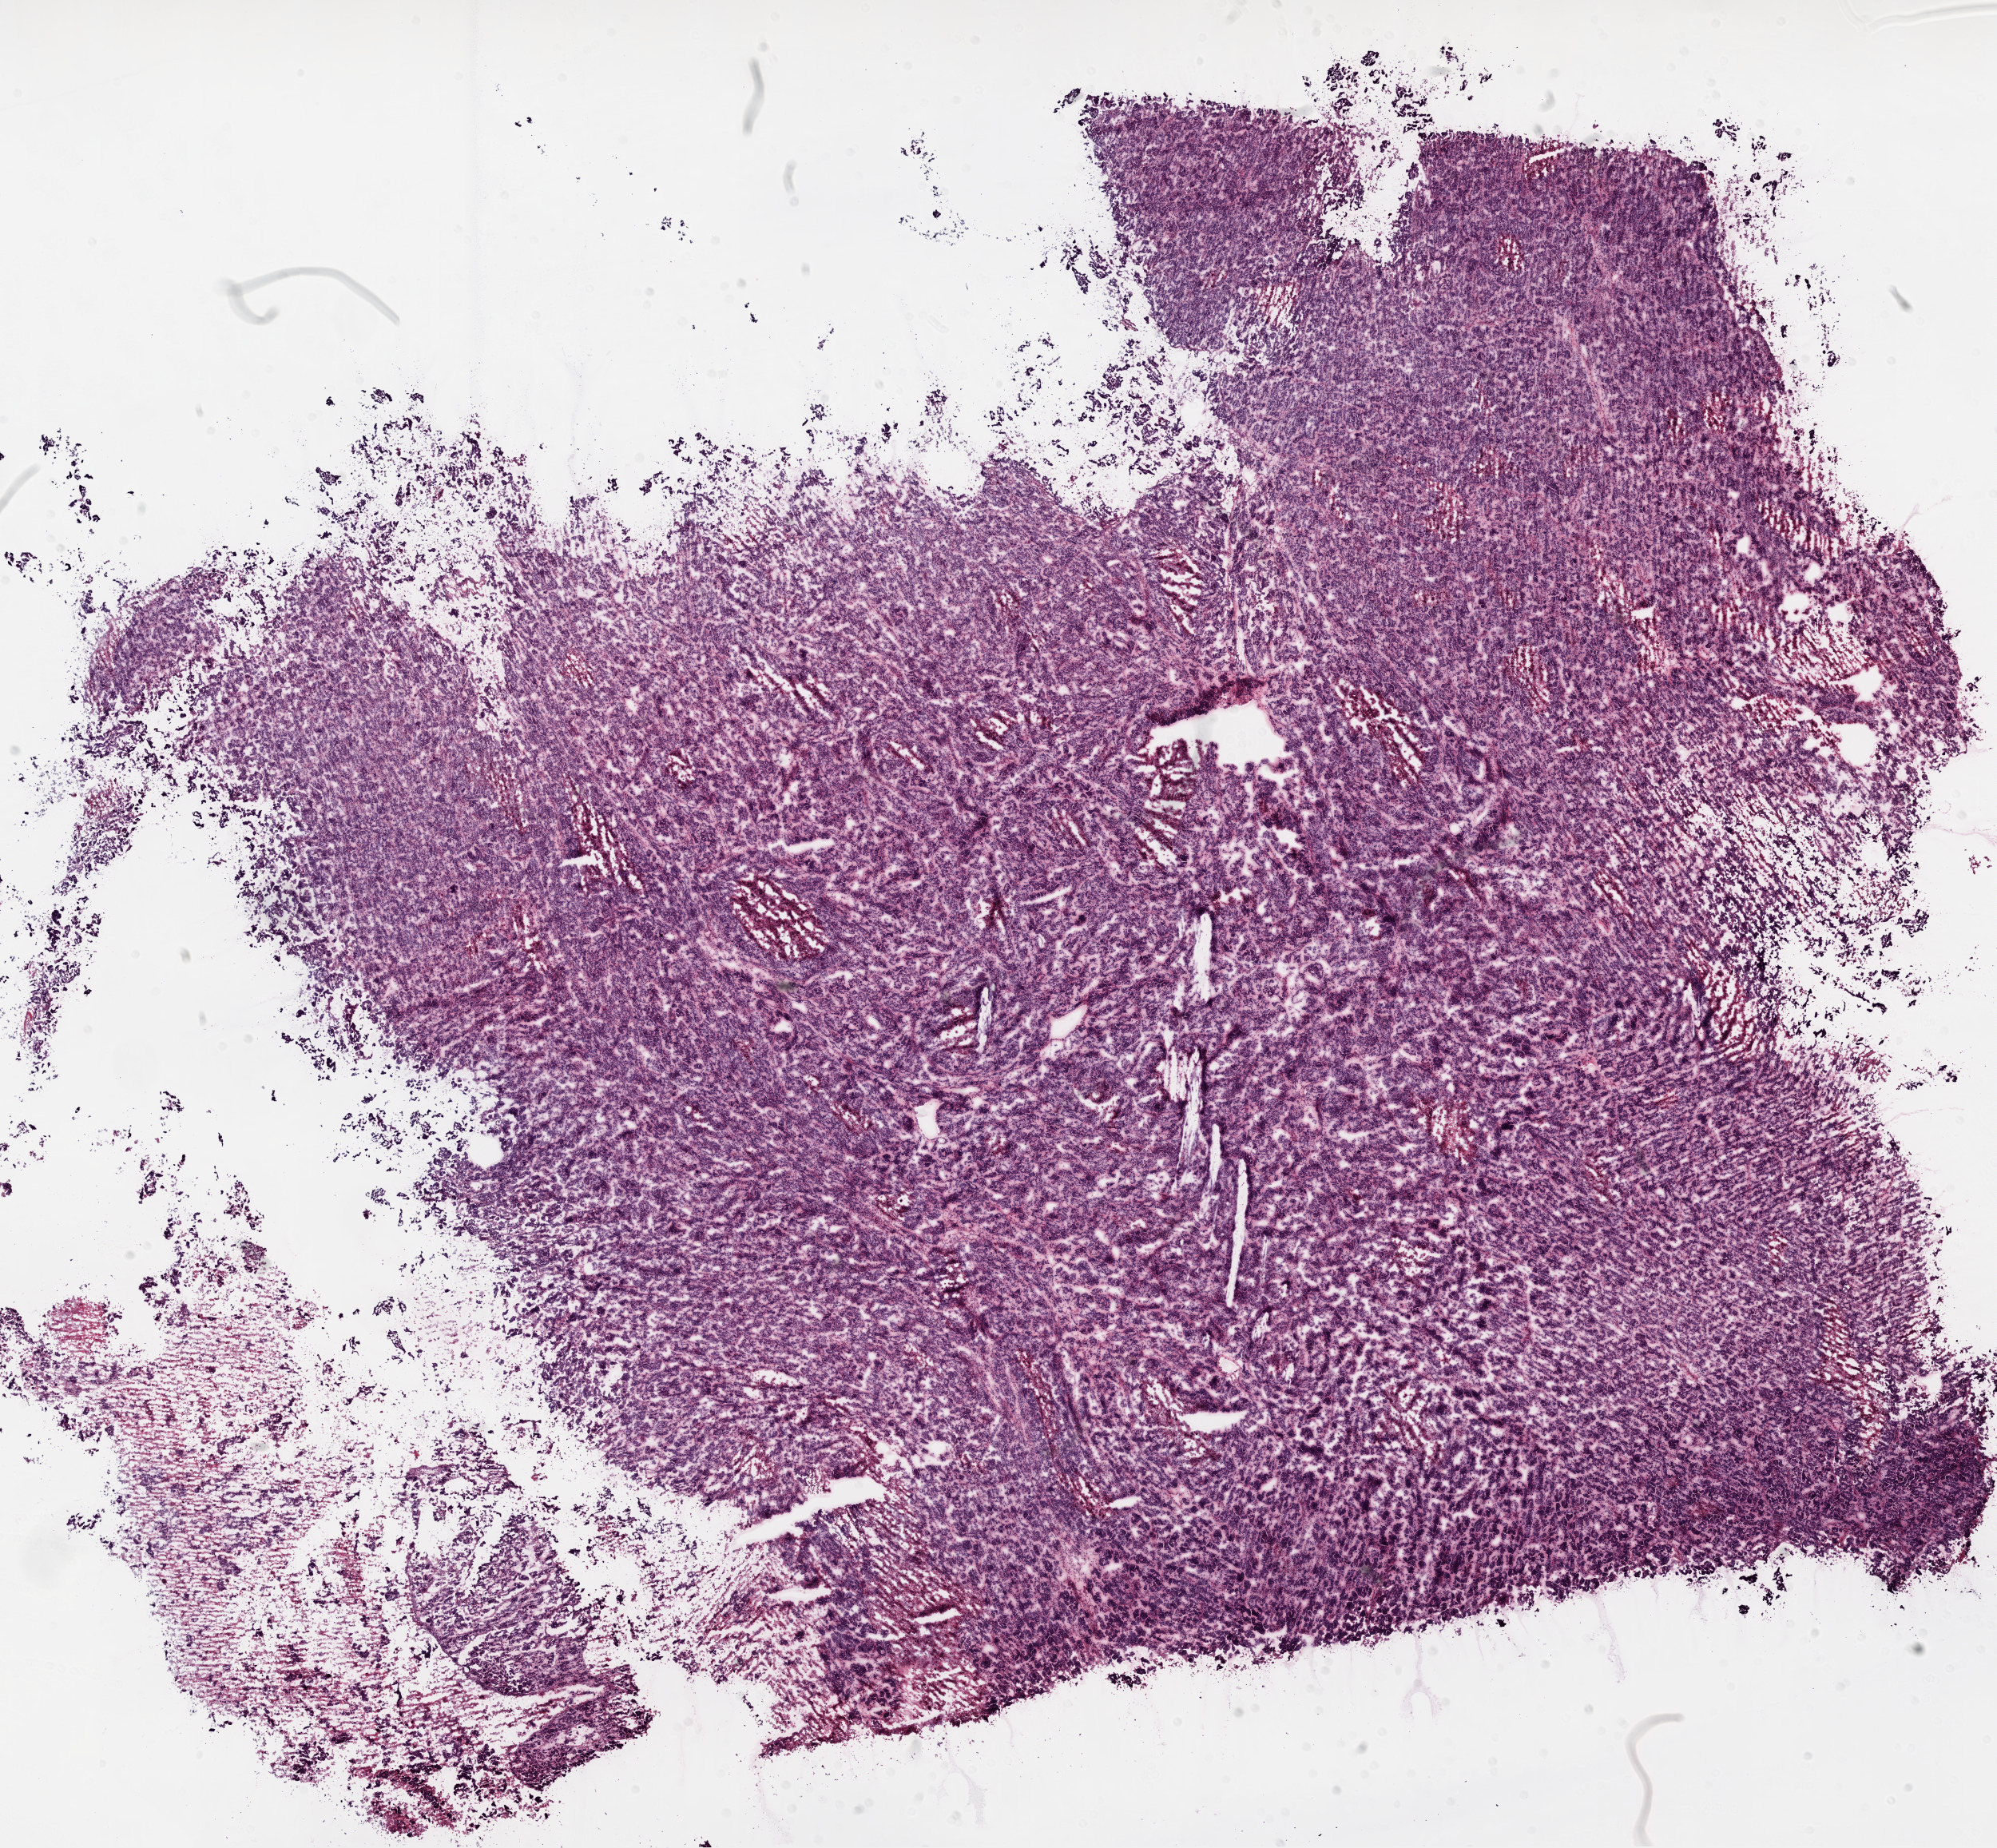
Digitized Hematoxylin and eosin (H&E) stained tissue section (whole slide) — a low-resolution overview of the entire scanned area, about 20.1 x 18.6 mm. Frozen section. Ovary, primary tumour sample. Female, age 49 years at initial diagnosis. Histologic grade: G3 (poorly differentiated). Pathologist review of this section (percent, as recorded): tumour cells 94%, tumour nuclei 99%, normal cells 0%, stromal cells 1%, necrosis 5%.
FIGO stage: IIIC. Pathologic diagnosis: Serous cystadenocarcinoma, NOS.